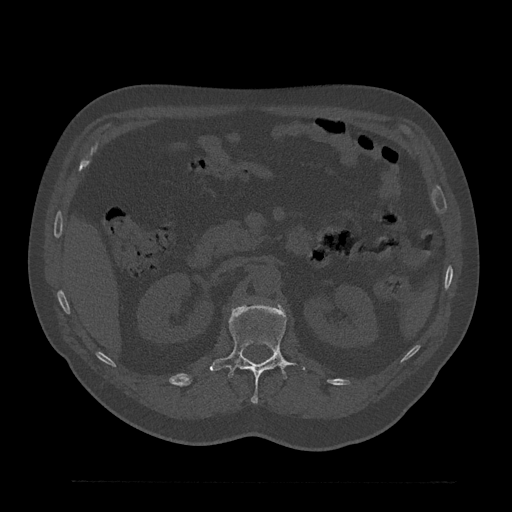
CT including the spine, one axial slice. Slice 163 of 797 in the series (ordered by position). 120 kVp. Bone window (W 1800 / L 400 HU). 512 × 512 image matrix, field of view 430 × 430 mm. Patient: male, 61 years. Case-level facts recorded for this patient, not image findings: primary cancer: prostate.
Structures marked on this image (semi-automatic segmentation, software-assisted and operator-edited):
- L1 vertebra: box from (x=210, y=303) to (x=305, y=403) px